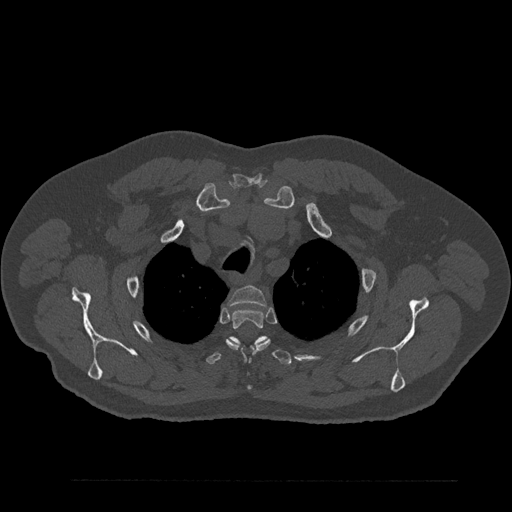
CT including the spine, one axial slice; position 679 of 797 along the scan axis; 120 kVp; bone window (W 1800 / L 400 HU); 512 × 512 image matrix, field of view 430 × 430 mm. Patient: male, 61 years. From the clinical record (not read from this slice): primary cancer: prostate.
Annotated regions visible in this slice (semi-automatic segmentation, software-assisted and operator-edited):
- T2 vertebra: bounding box <229,286,266,306> (left, top, right, bottom; pixels)
- T3 vertebra: <226,309,270,389>
- T4 vertebra: <206,336,292,365>